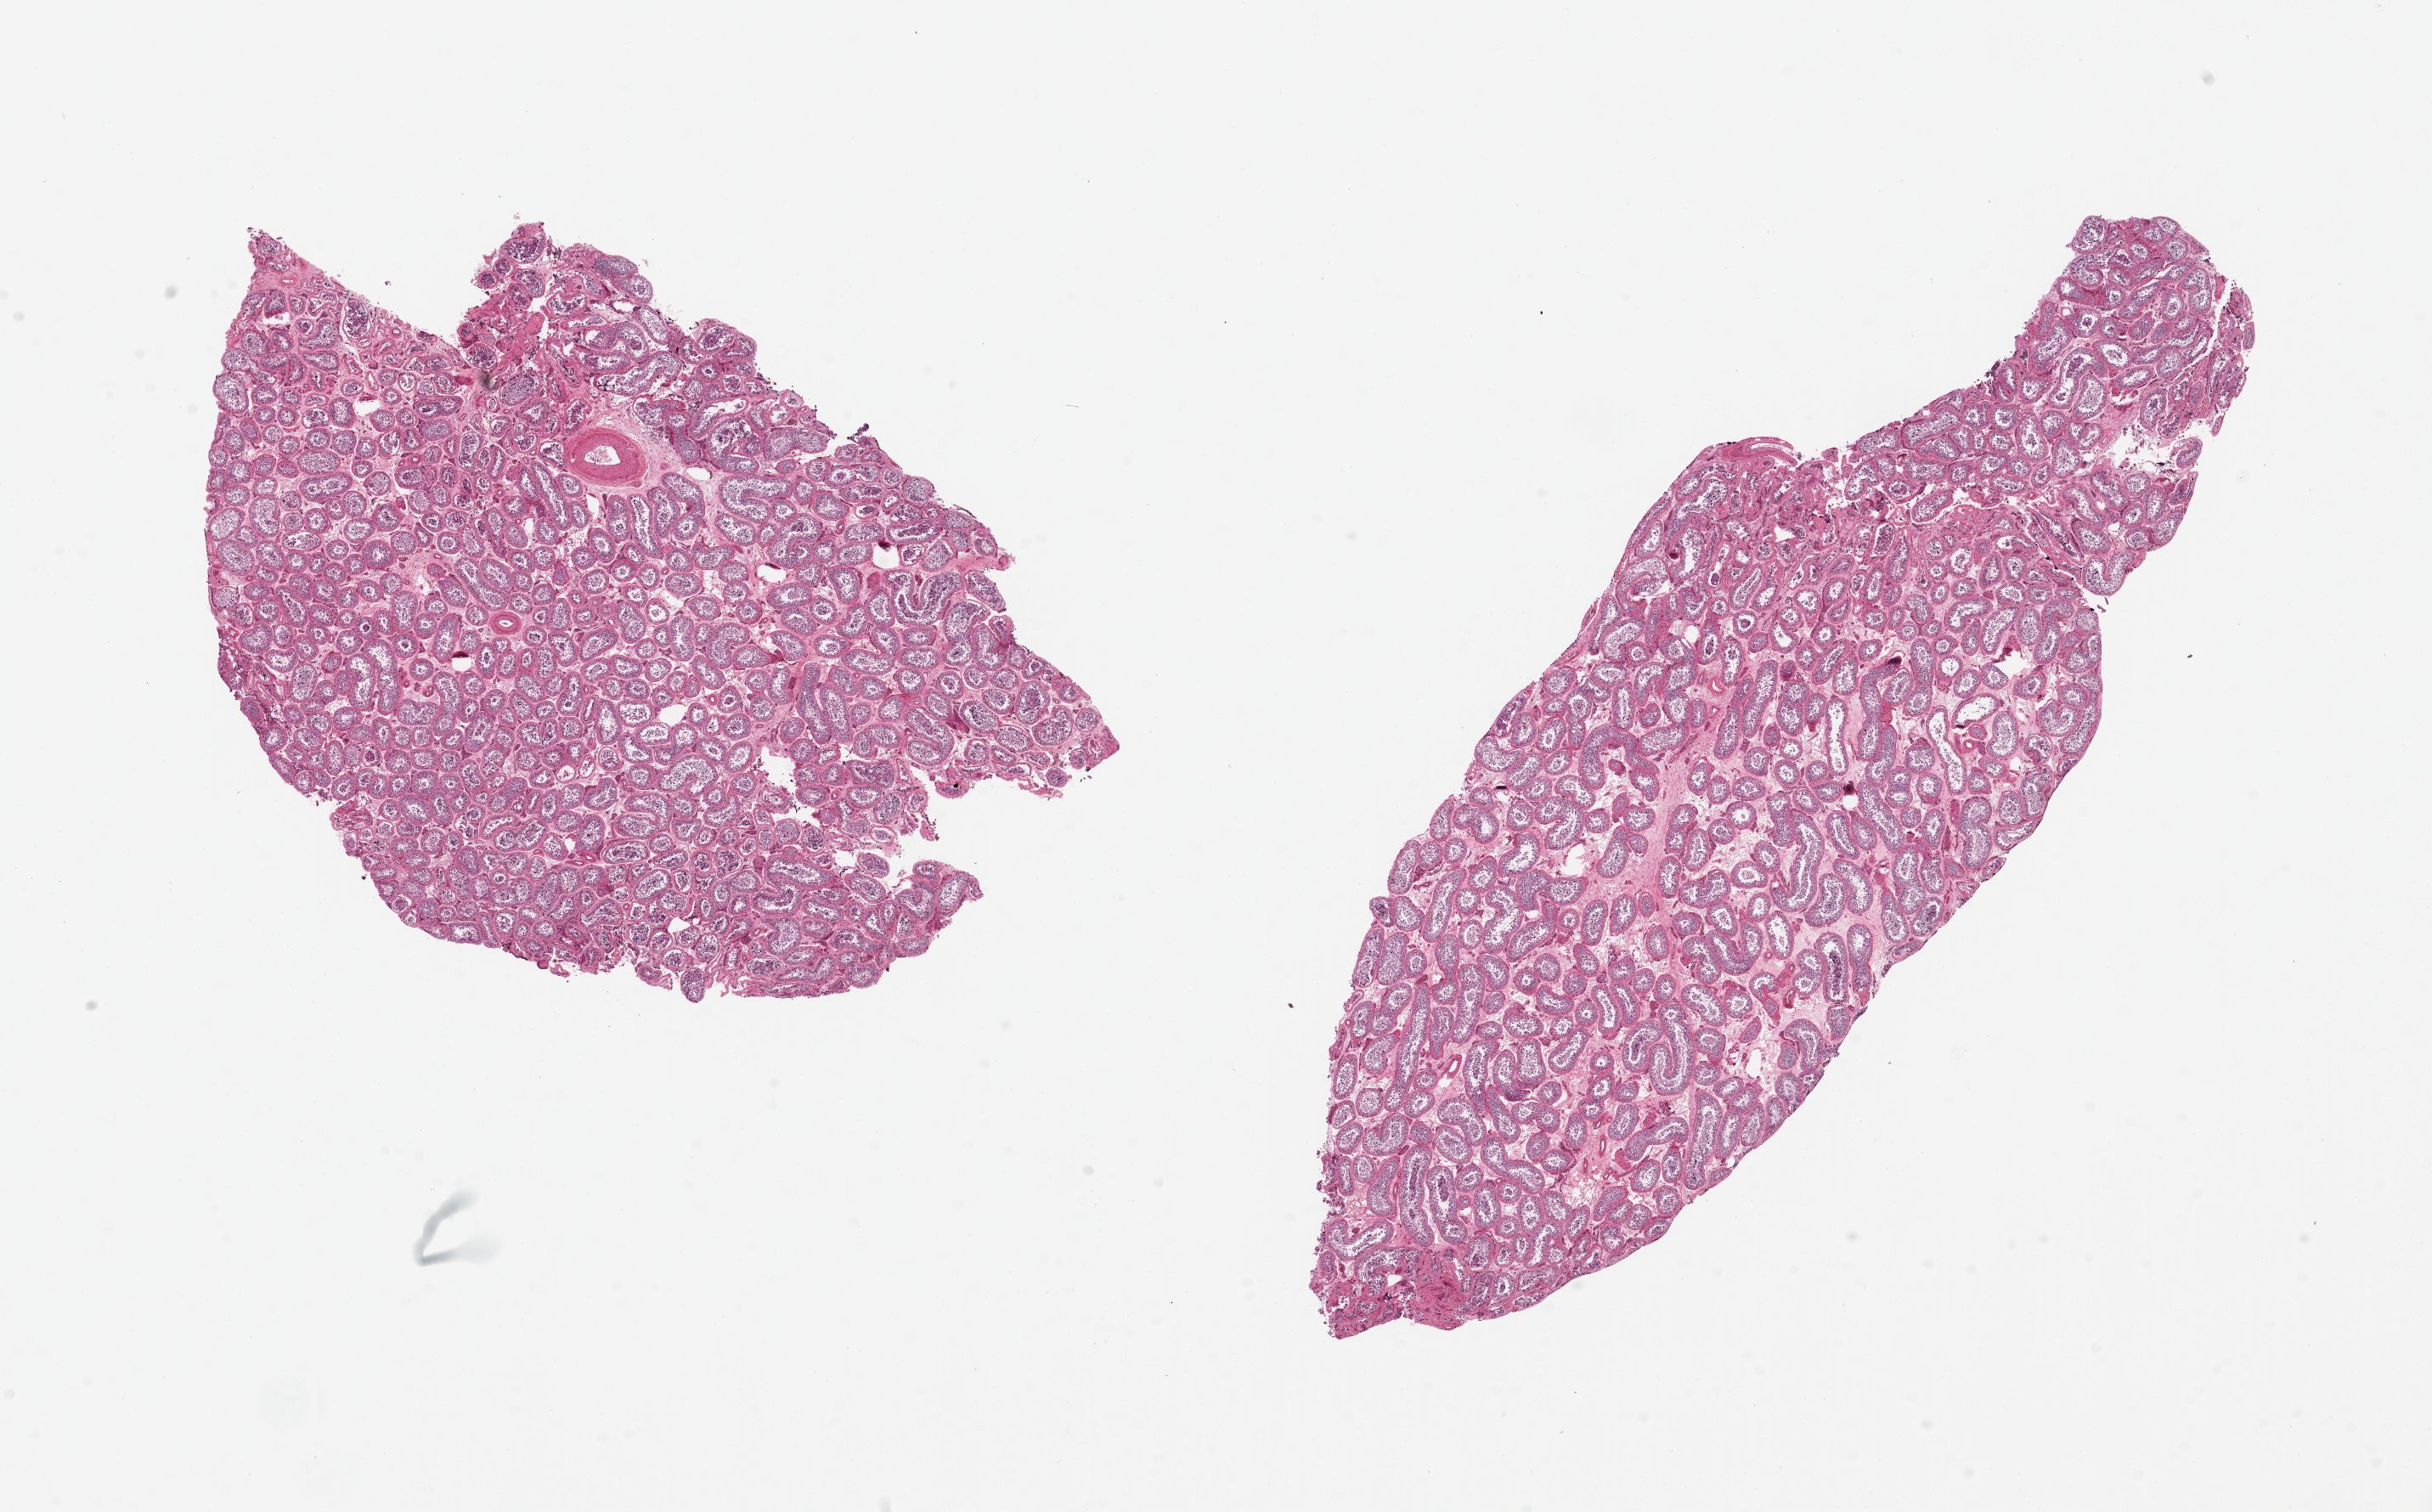
Whole-slide image, haematoxylin and eosin stain, shown as a low-resolution overview of the whole scanned area (about 22.6 x 14.1 mm, slide scanned at 20x), PAXgene-fixed paraffin-embedded (PFPE) section, sampled site (target tissue): testis, tissue donor sample. Donor sex: male.
• reviewer comment on this tissue sample: 2 pieces. ~10x6mm, Spertmatogenesis is present